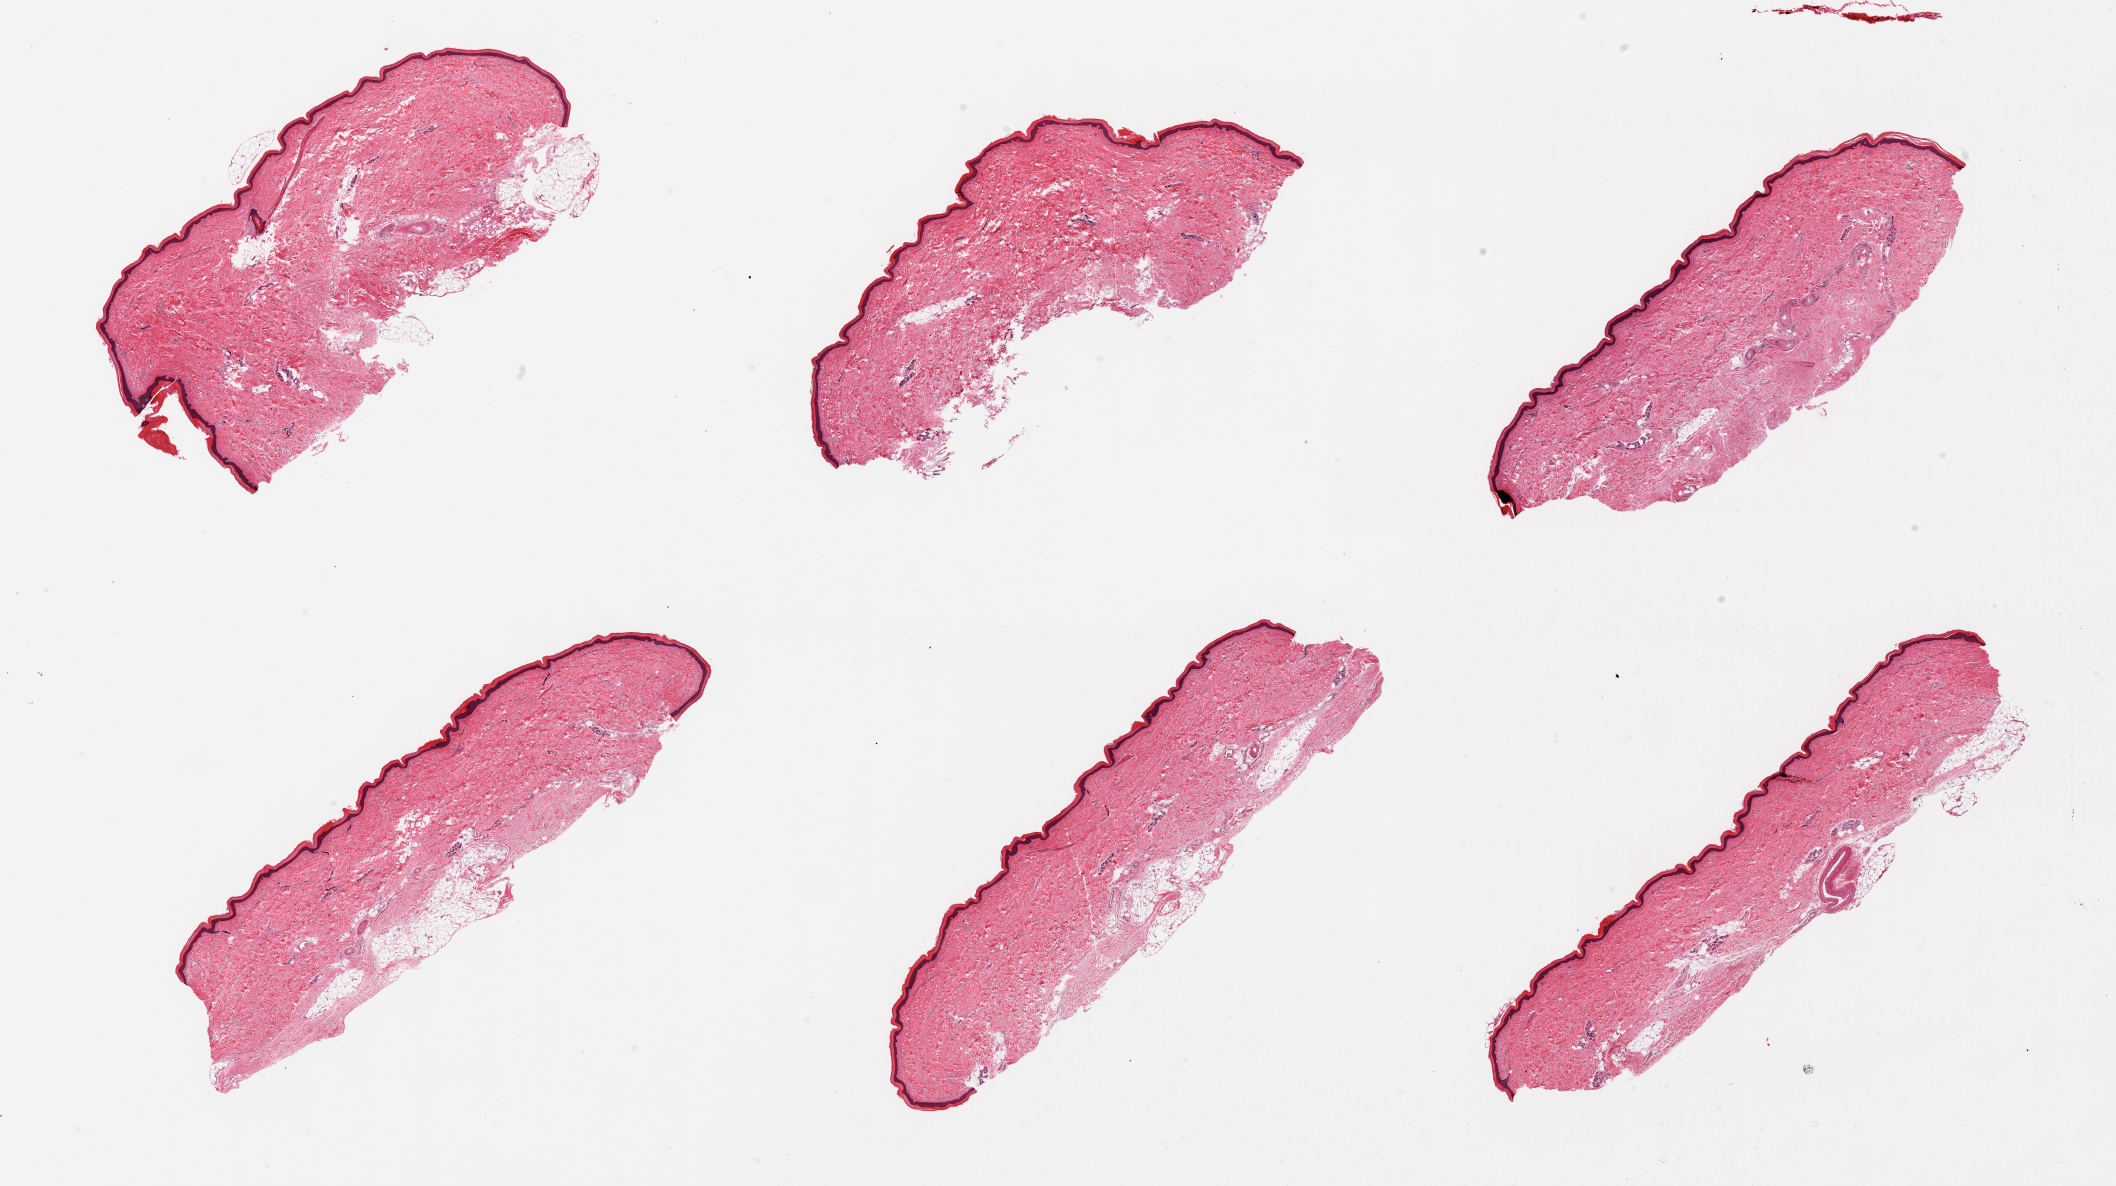
H&E whole-slide image — low-resolution overview of the scanned area, about 33.5 x 18.8 mm (from a 20x scan), PAXgene-fixed paraffin-embedded (PFPE) section, section of skin of lower leg (target tissue), donor tissue sample.
• reviewer comment on this tissue sample: 6 pieces; 46um thick epidermis; up to 10% internal and external fat; compact keratosis